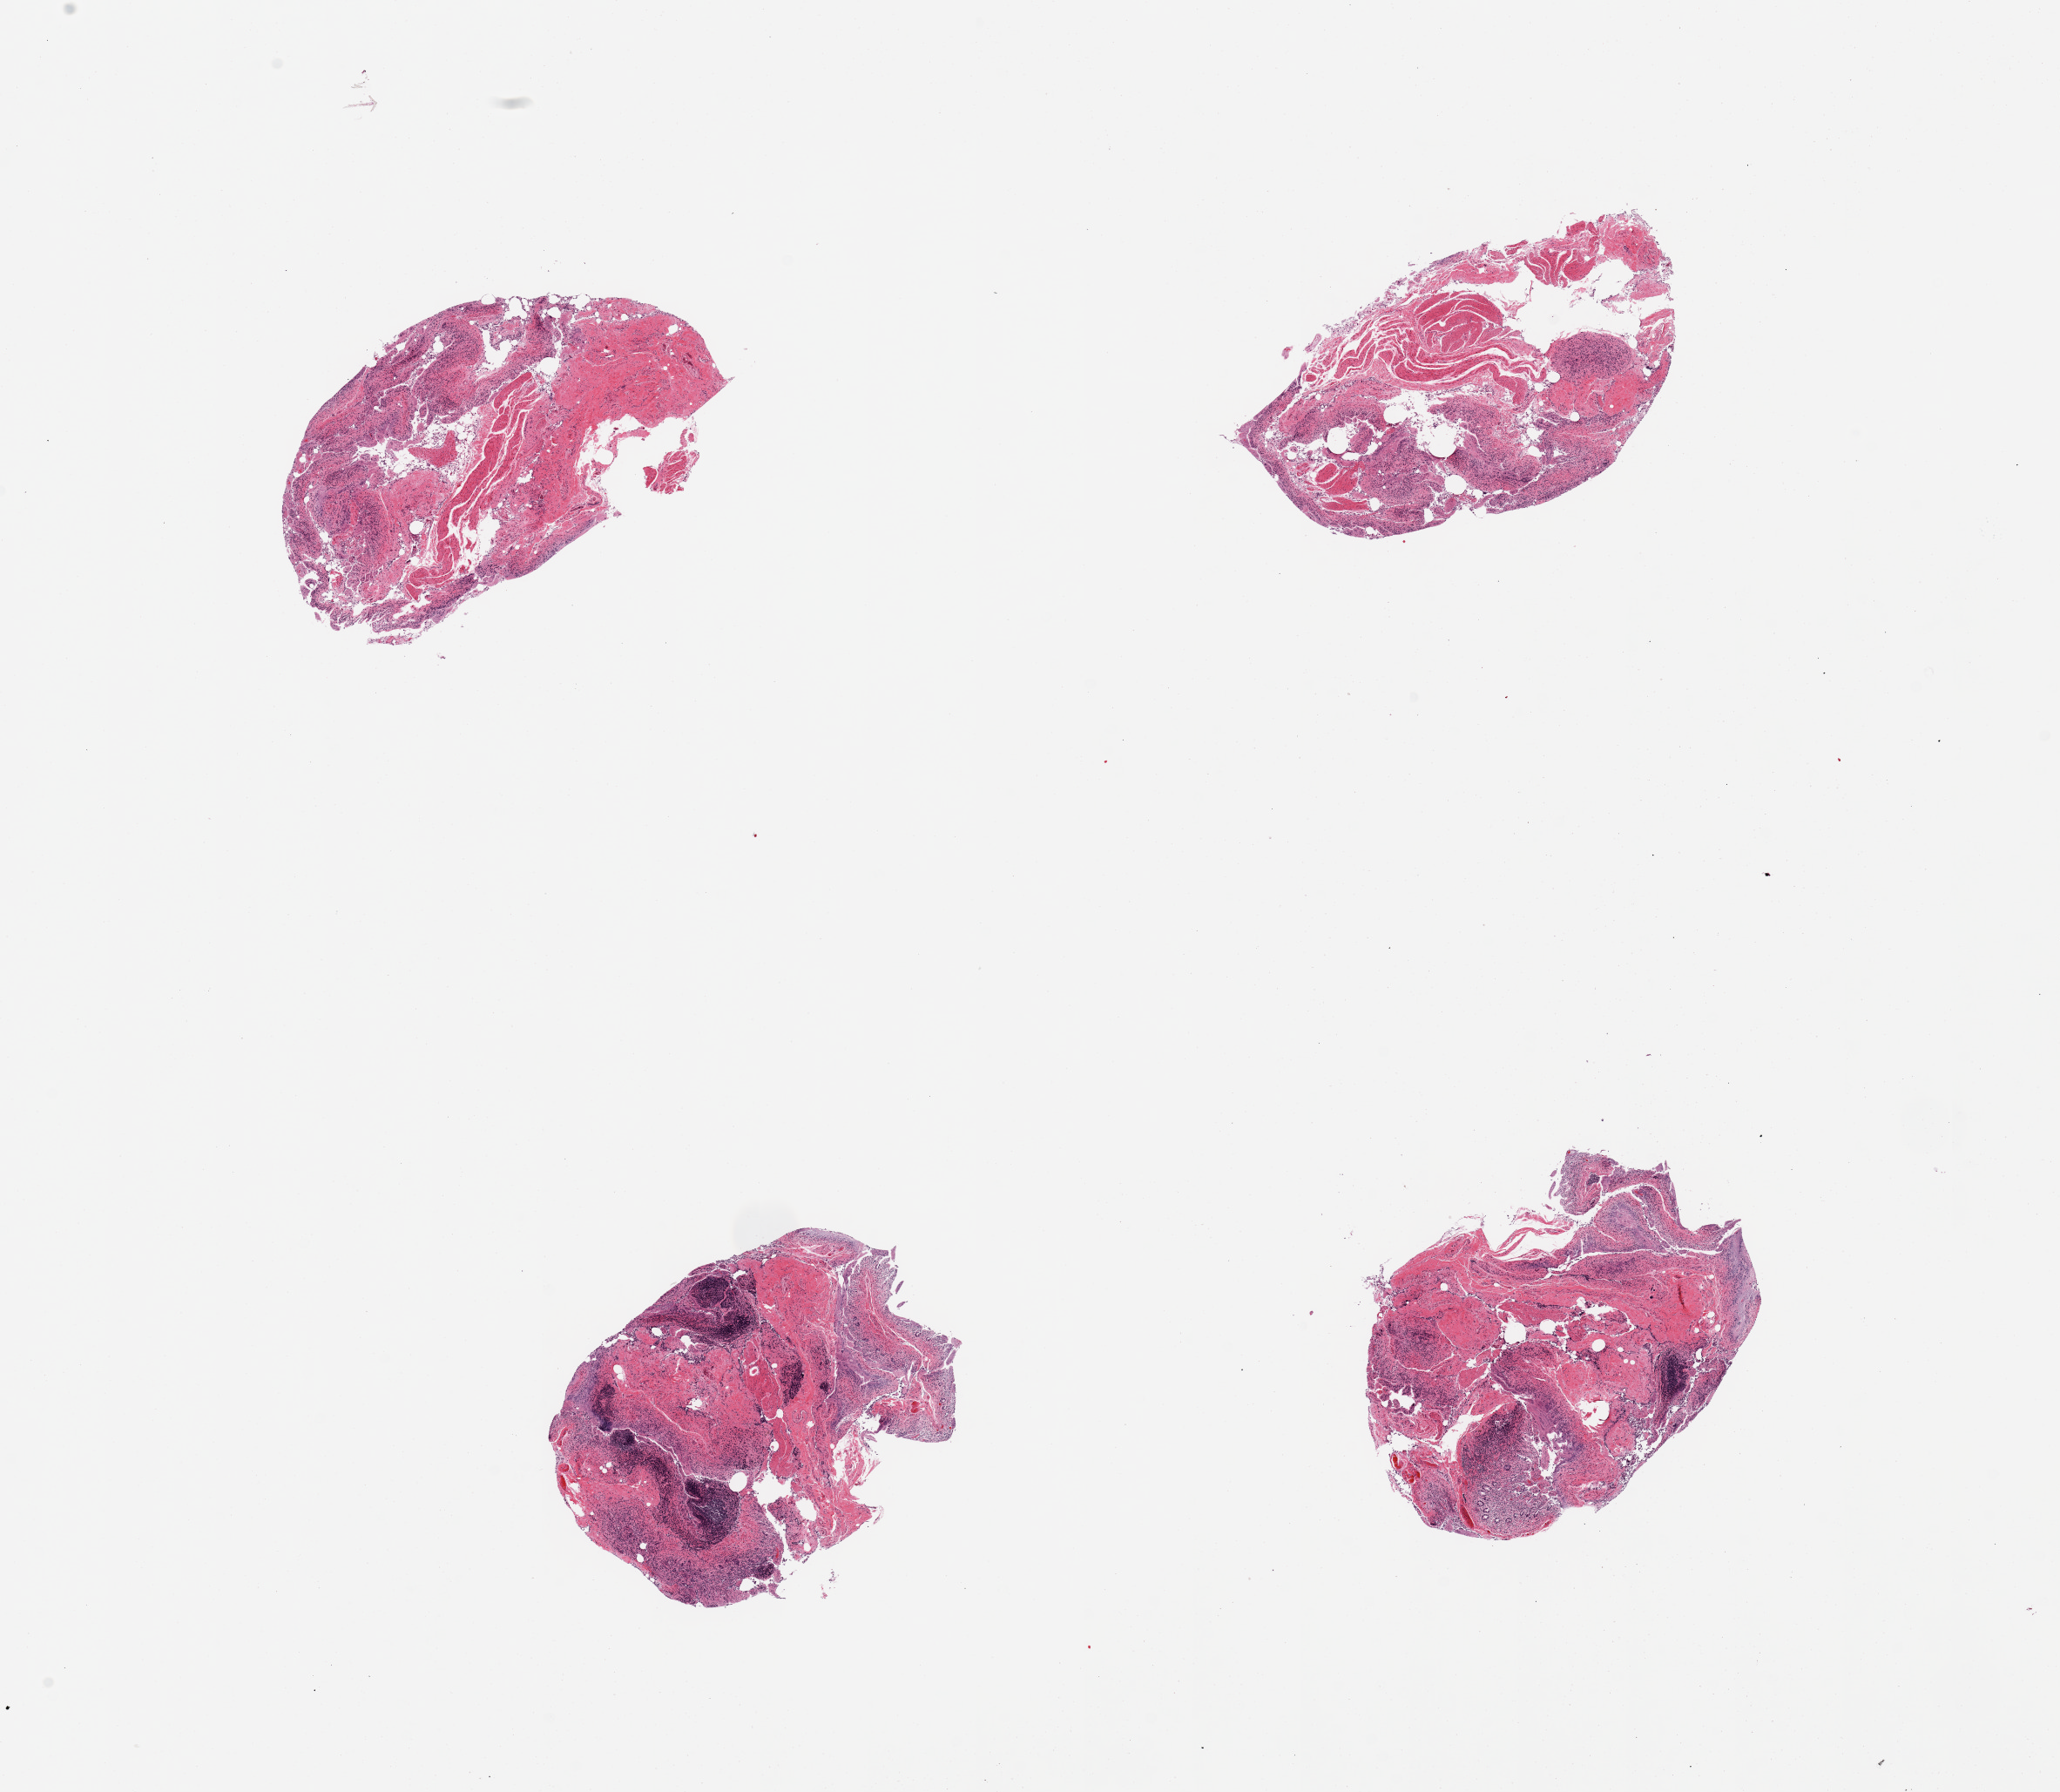
Digitized haematoxylin and eosin-stained section — whole scanned area (about 18.7 x 16.3 mm) shown as a low-resolution overview, PAXgene-fixed paraffin-embedded (PFPE) section, section of ileum (target tissue), tissue donor sample. Donor: female.
Pathologist's review note for this sample: 4 pieces, ~10% lymphoid/Peyer's aggregates, but badly autolyzed.